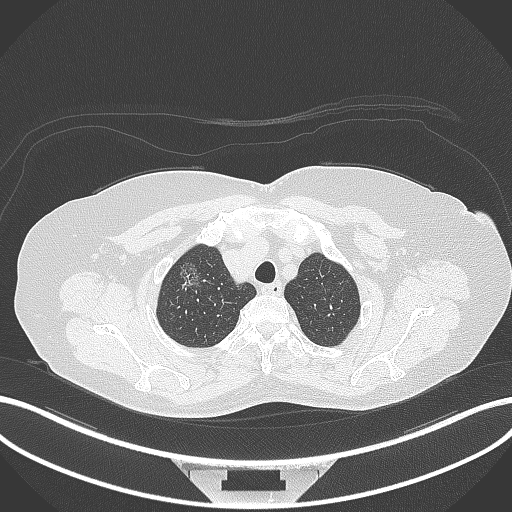
Chest CT, one axial slice; slice 303 of 365 in the series (ordered by position); reconstruction kernel B70f; 120 kVp; lung window (W 1500 / L -600 HU); 512 × 512 image matrix. Female patient, age 62 years. From the clinical record (not read from this slice): clinical TNM (as recorded): T1c N0 M0.
Structures marked on this image (rectangle marked by the reading radiologist):
- lung tumour (recorded histology: adenocarcinoma): bounding box (x1, y1, x2, y2) in pixels: (177, 257, 210, 293)